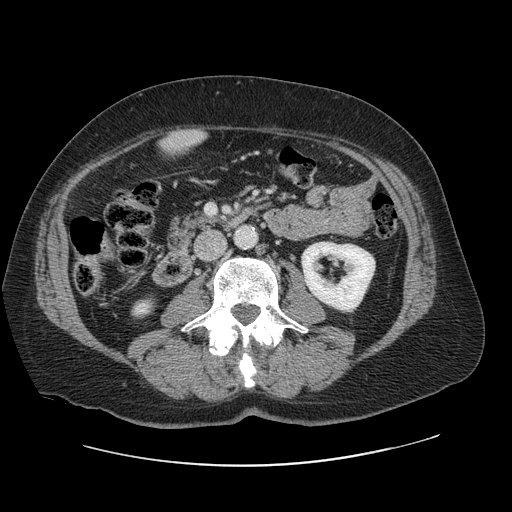
Contrast-enhanced abdominal CT, one axial slice; position 14 of 138 along the scan axis; intravenous contrast given; soft-tissue window (W 400 / L 40 HU); 512 × 512 image matrix, field of view 402 × 402 mm. Male patient, age 71 years. Case-level facts recorded for this patient, not image findings: diagnosis: colorectal cancer liver metastases, imaged before liver resection; multiple liver metastases: no; largest metastasis: 3.3 cm; disease in both lobes: no.
Annotated regions visible in this slice (expert manual segmentation):
- liver: box from (x=162, y=131) to (x=203, y=156) px